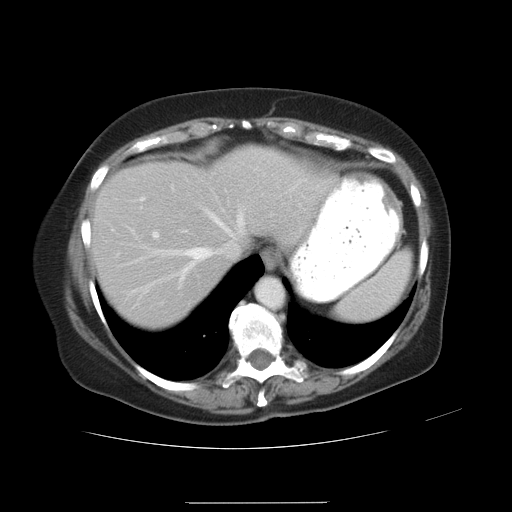
Contrast-enhanced abdominal CT, one axial slice; slice 25 of 32 in the series (ordered by position); 120 kVp; intravenous contrast given; soft-tissue window (W 400 / L 40 HU); 512 × 512 image matrix, field of view 386 × 386 mm. Female patient, age 65 years. Case-level facts recorded for this patient, not image findings: diagnosis: colorectal cancer liver metastases, imaged before liver resection; multiple liver metastases: yes; largest metastasis: 1.7 cm.
Annotated regions visible in this slice (expert manual segmentation):
- hepatic veins: bounding box <120,185,246,295> (left, top, right, bottom; pixels)
- liver: <93,147,323,326>
- planned liver remnant (the part of the liver to remain after resection): <93,164,241,326>
- portal vein (with intrahepatic branches): <152,229,159,239>